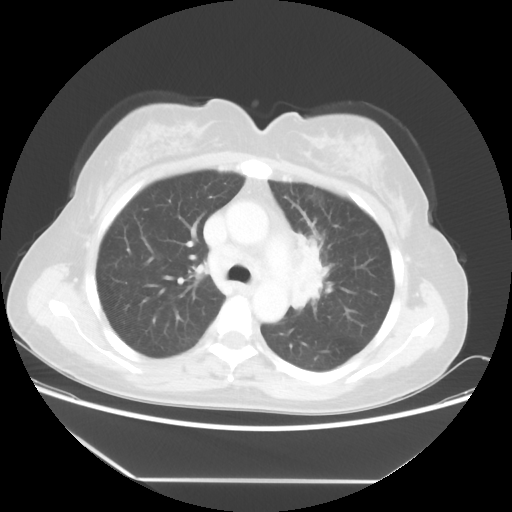
Chest CT, one axial slice. Position 35 of 52 along the scan axis. Reconstruction kernel STANDARD. 100 kVp. Lung window (W 1500 / L -600 HU). 512 × 512 image matrix, field of view 390 × 390 mm. Patient: female, 50 years. From the clinical record (not read from this slice): clinical TNM (as recorded): T2 N3 M0.
Annotated regions visible in this slice (bounding box drawn by a radiologist):
- lung tumour (recorded histology: adenocarcinoma): bounding box [x1, y1, x2, y2] px = [284, 215, 342, 318]